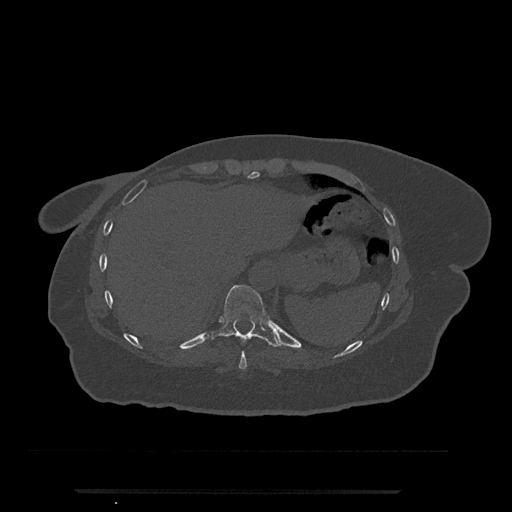
CT including the spine, one axial slice. Slice 300 of 797 in the series (ordered by position). Bone window (W 1800 / L 400 HU). 0.5 mm slice thickness. 512 × 512 image matrix, field of view 440 × 440 mm. Patient: female, 51 years. Case-level facts recorded for this patient, not image findings: primary cancer: neuro.
Structures marked on this image (semi-automatic segmentation, software-assisted and operator-edited):
- T10 vertebra: box from (x=212, y=285) to (x=279, y=347) px
- T9 vertebra: (x=238, y=351)–(x=247, y=370)